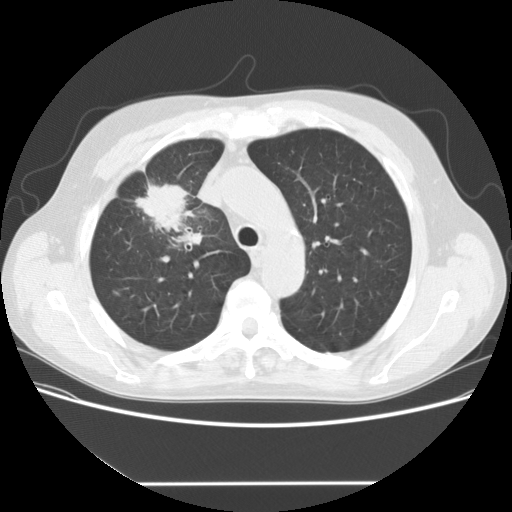
Low-dose screening chest CT, one axial slice; position 114 of 153 along the scan axis; reconstruction kernel STANDARD; lung window (W 1500 / L -600 HU); 2.5 mm slice thickness; 512 × 512 image matrix.
Structures marked on this image (expert manual segmentation):
- lesion 1 (tumor, upper lobe of right lung): bounding box (x1, y1, x2, y2) in pixels: (135, 184, 195, 232)